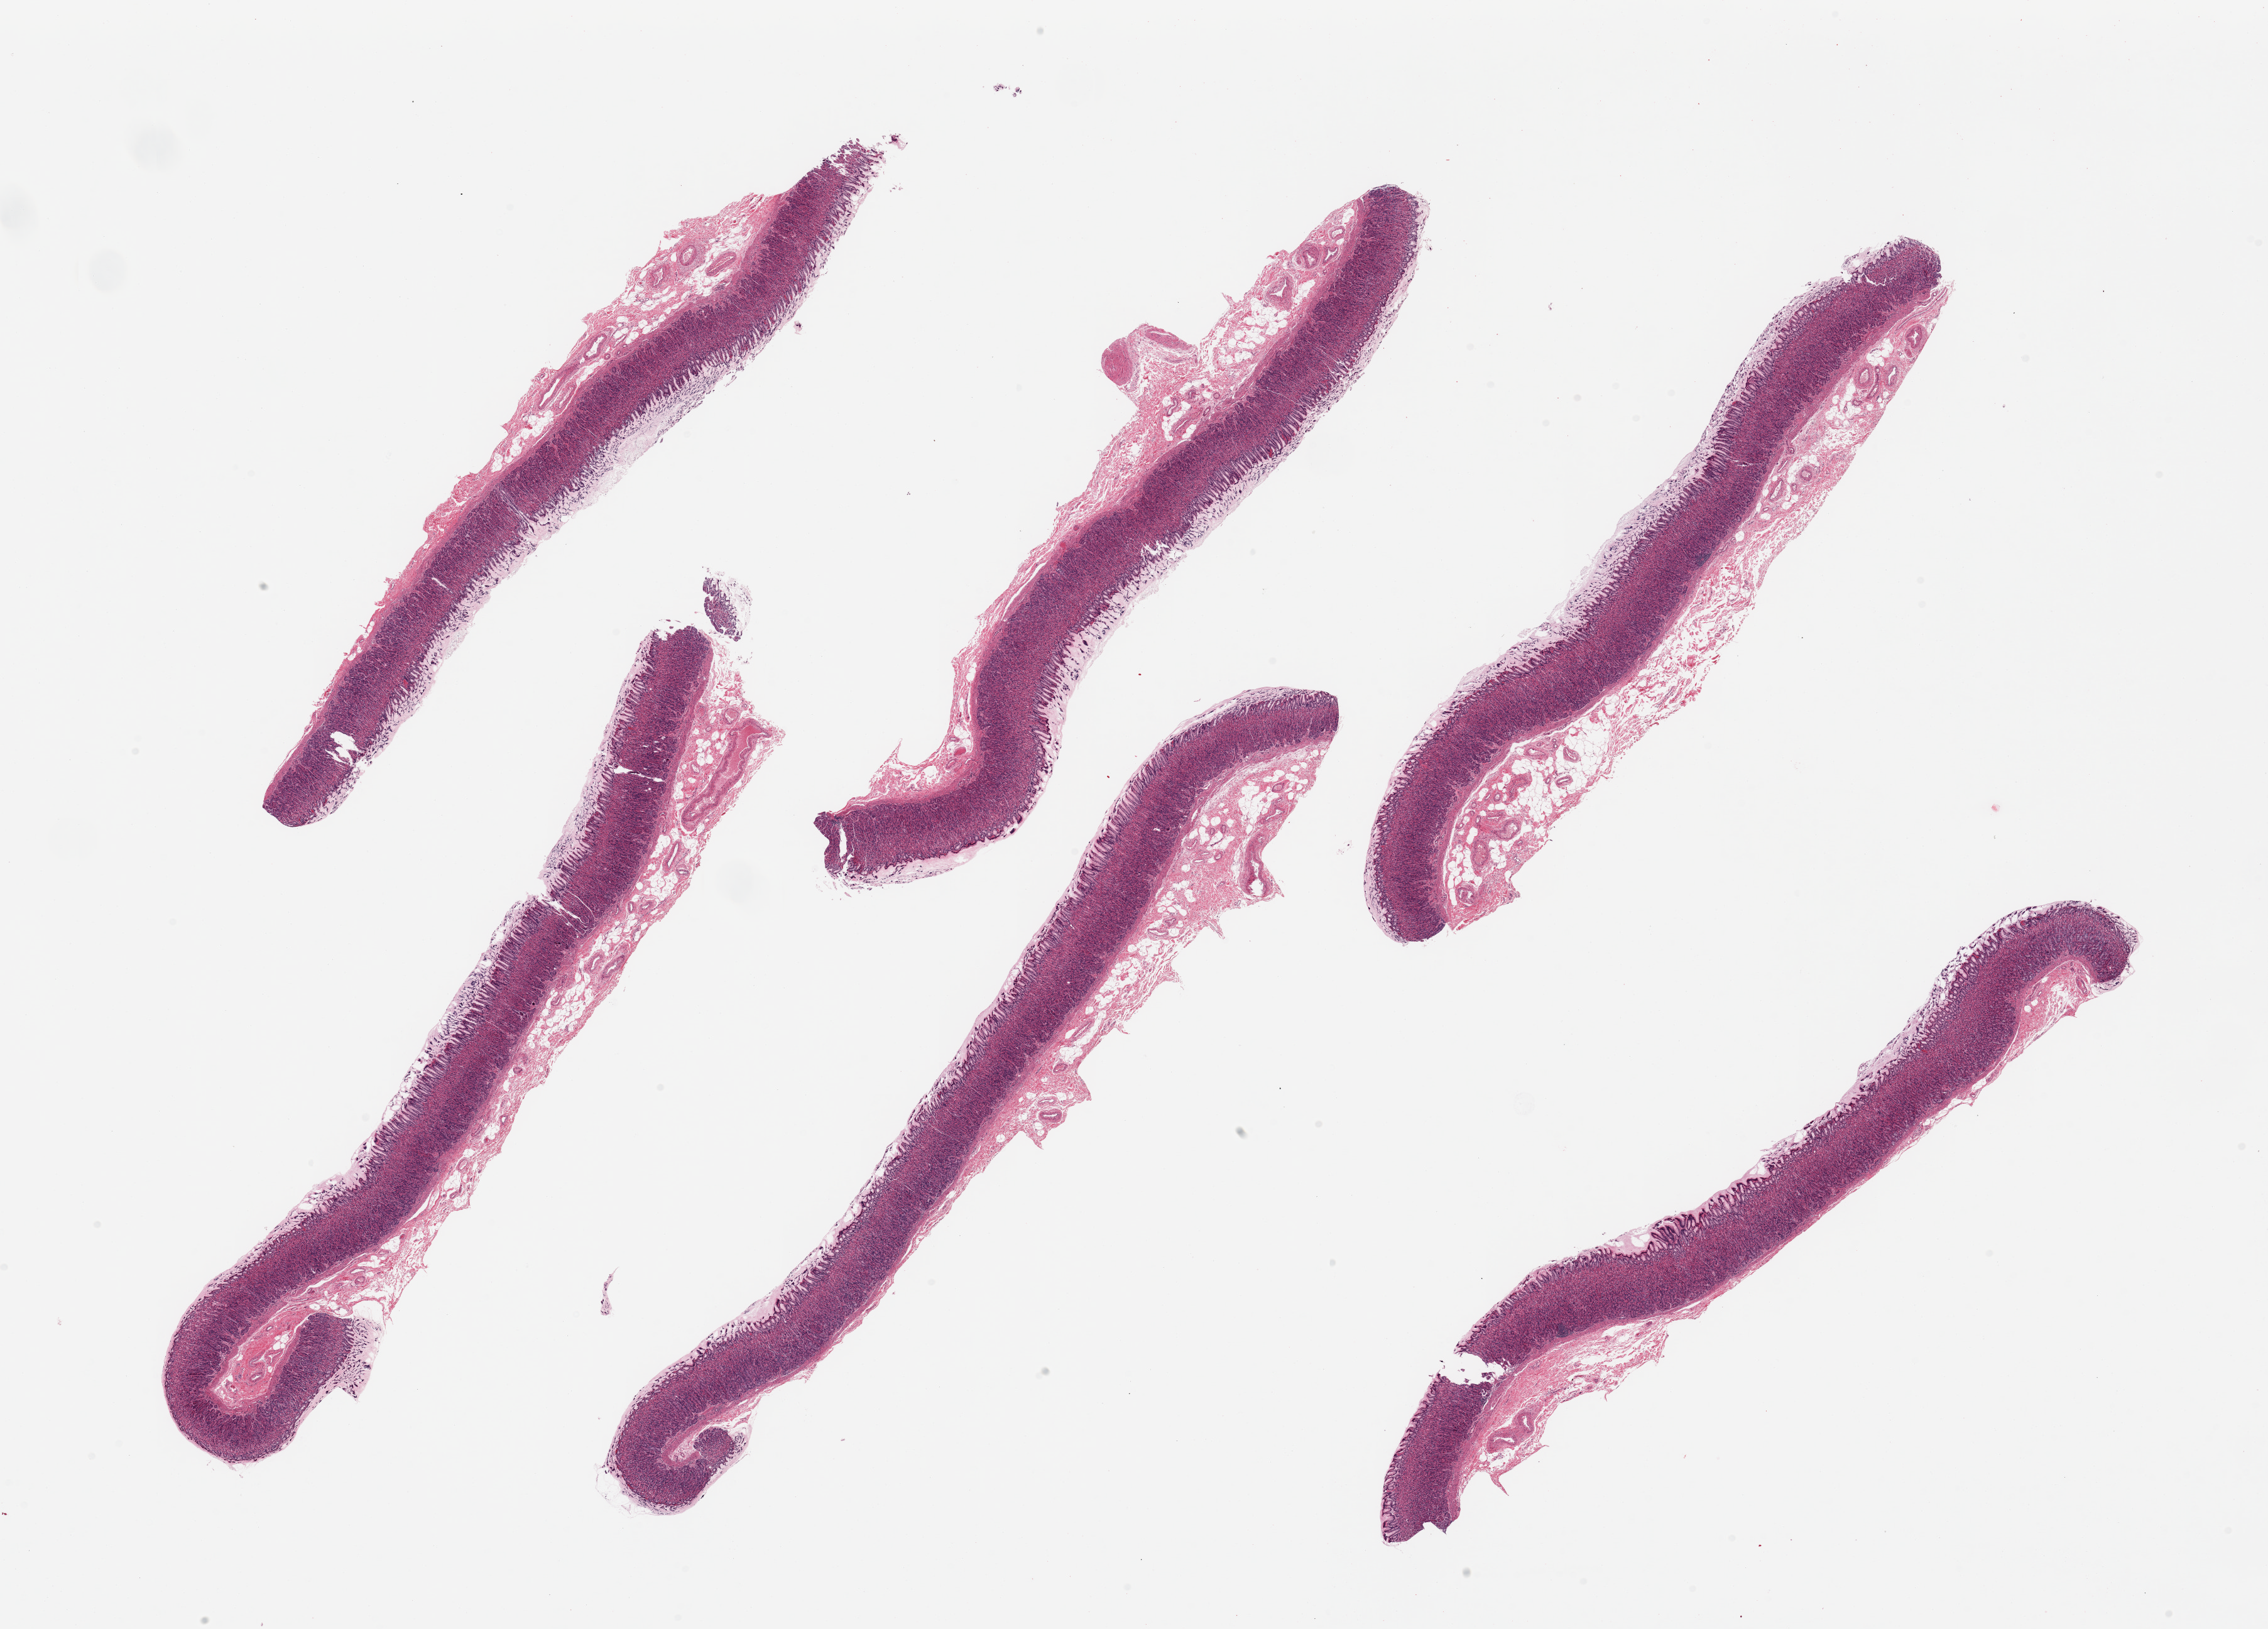
Digitized H&E-stained section — low-resolution overview of the scanned area, about 28.5 x 20.5 mm (from a 20x scan), PAXgene-fixed, paraffin-embedded tissue, target tissue: stomach, donor tissue sample. Female donor.
Reviewer comment on this tissue sample: 6 pieces, well preserved mucosa, ~70-80% thickness, valuable specimen.